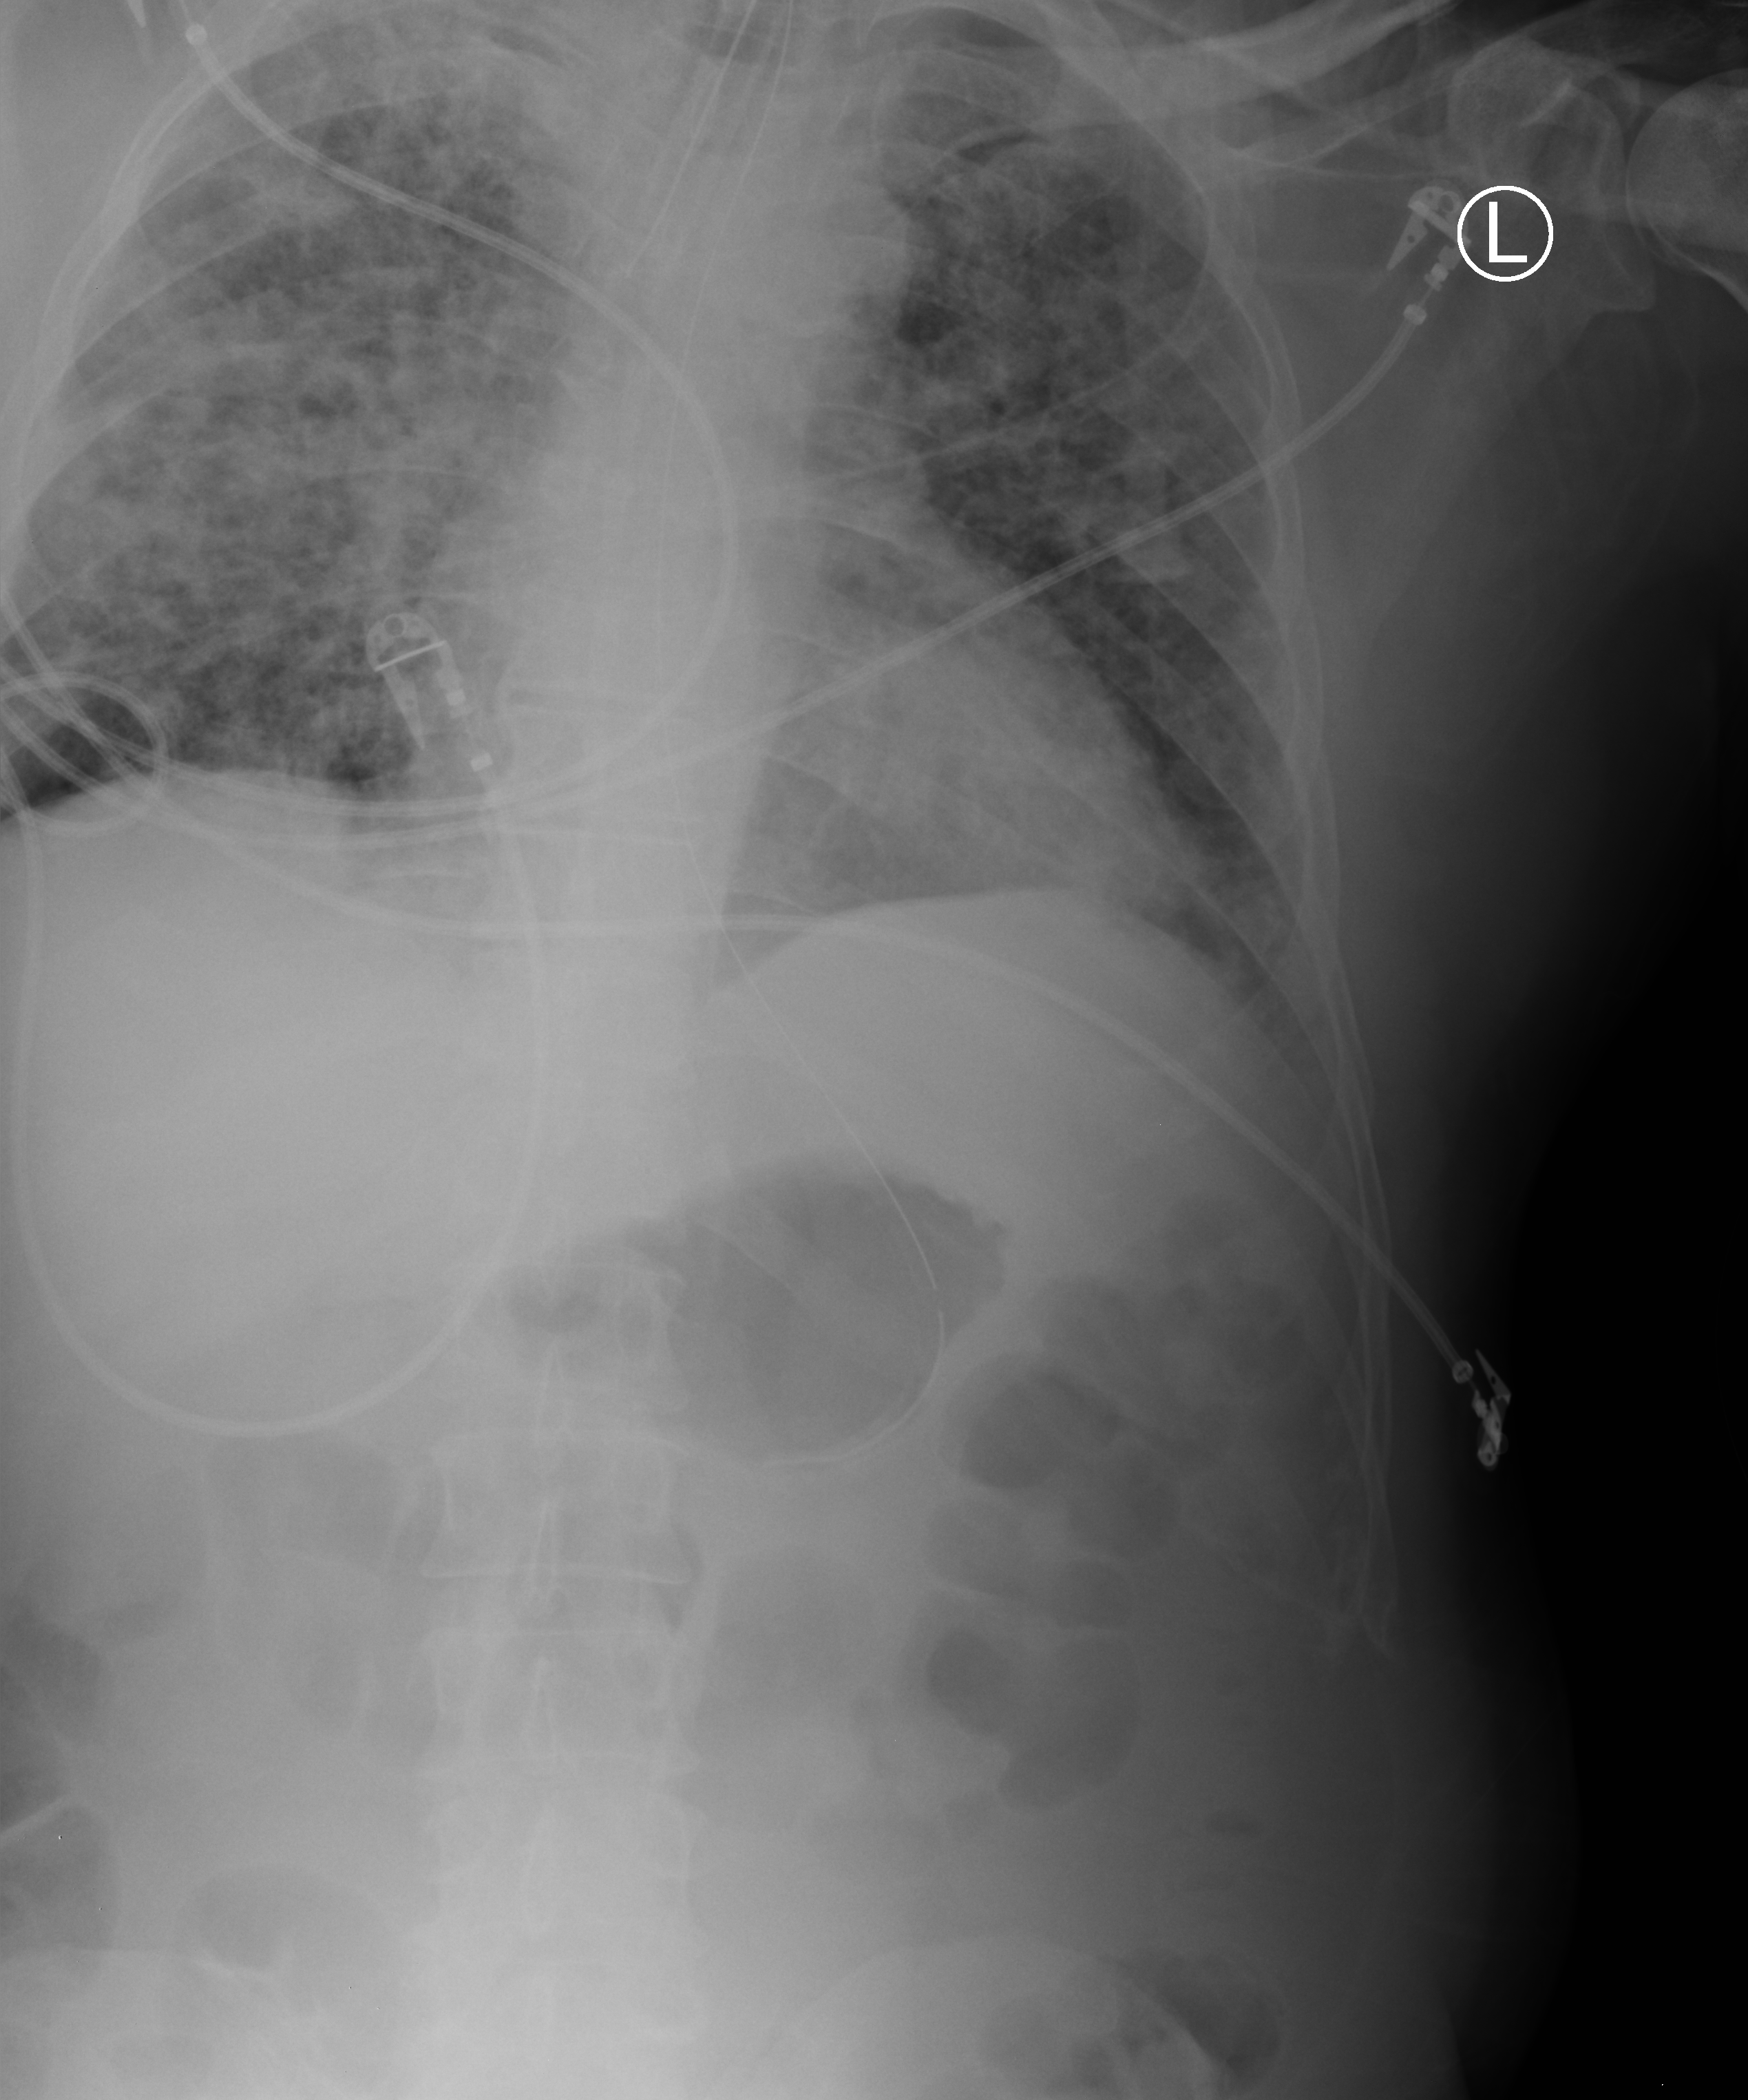
Portable chest radiograph, anteroposterior (AP) projection. Male patient hospitalised with COVID-19, age 18–59 years.
Hospital-stay facts (about this admission, not read from this image; timing relative to this image not recorded): mechanically ventilated during this hospital stay: yes; admitted to intensive care during this hospital stay: yes.